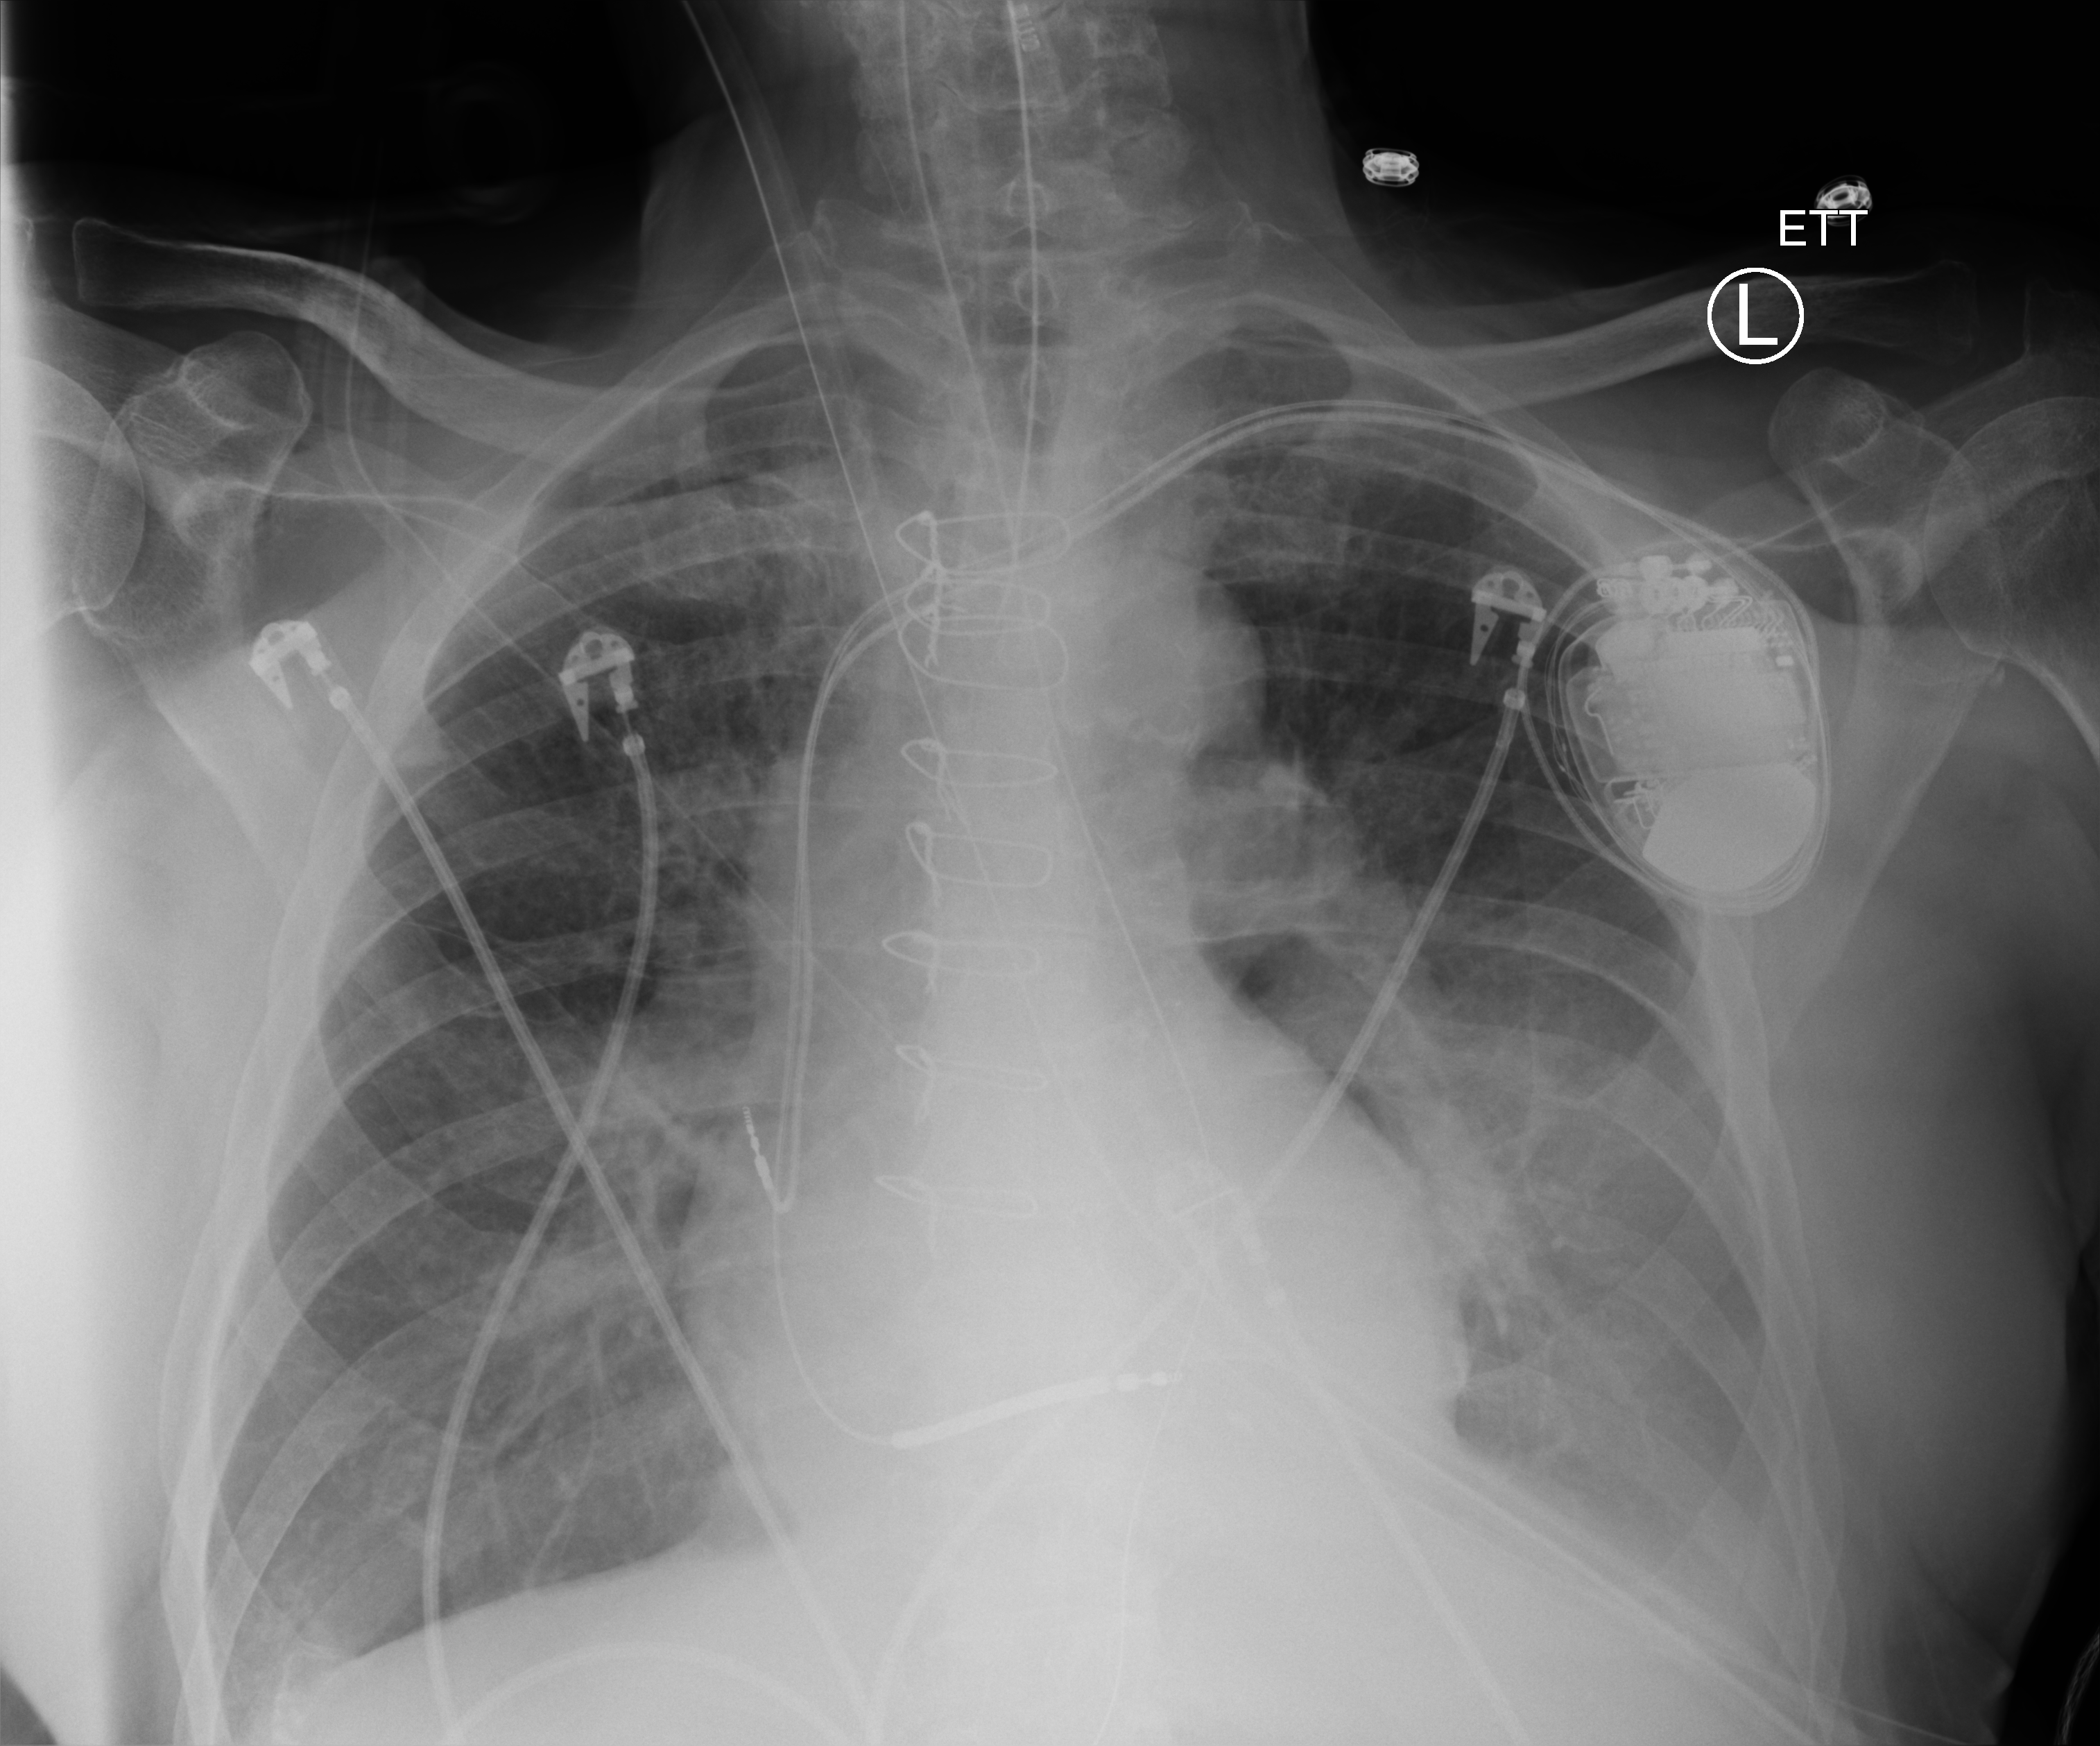
Chest X-ray (portable); anteroposterior (AP) projection. Male patient hospitalised with COVID-19, age 75–90 years.
From the hospital-stay record, not from the radiograph (when in the stay this image was taken is not recorded):
- mechanically ventilated during this hospital stay: yes
- admitted to intensive care during this hospital stay: yes
- length of hospital stay: 11 days